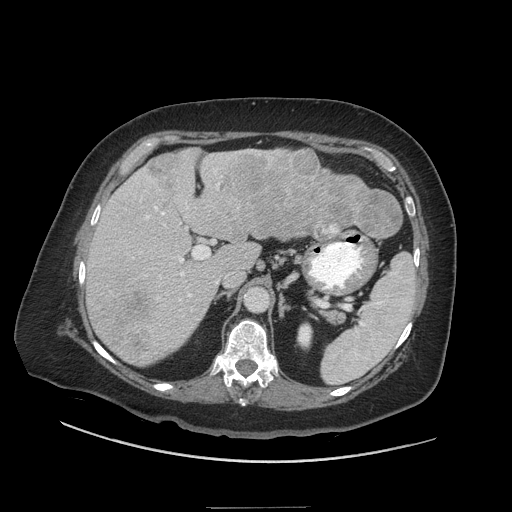
Contrast-enhanced abdominal CT (liver protocol), one axial slice. Slice 27 of 81 in the series (ordered by position). Reconstruction kernel STANDARD. 140 kVp. Soft-tissue window (W 400 / L 40 HU). 2.5 mm slice thickness. 512 × 512 image matrix, field of view 440 × 440 mm. Case-level facts recorded for this patient, not image findings: diagnosis: hepatocellular carcinoma (patient treated with transarterial chemoembolisation; whether this scan precedes or follows treatment is not stated here); TNM stage (as recorded): Stage-II; Child-Pugh class: A; tumour differentiation: moderately differentiated; tumour size: 1.7 cm.
Outlined on this slice (semi-automatically segmented with operator editing):
- liver parenchyma outside the tumour (the mass and vessels are separate outlines, so this box may not span the whole liver): bounding box <86,148,385,366> (left, top, right, bottom; pixels)
- mass: <103,148,402,361>
- liver vessels: <121,150,252,331>